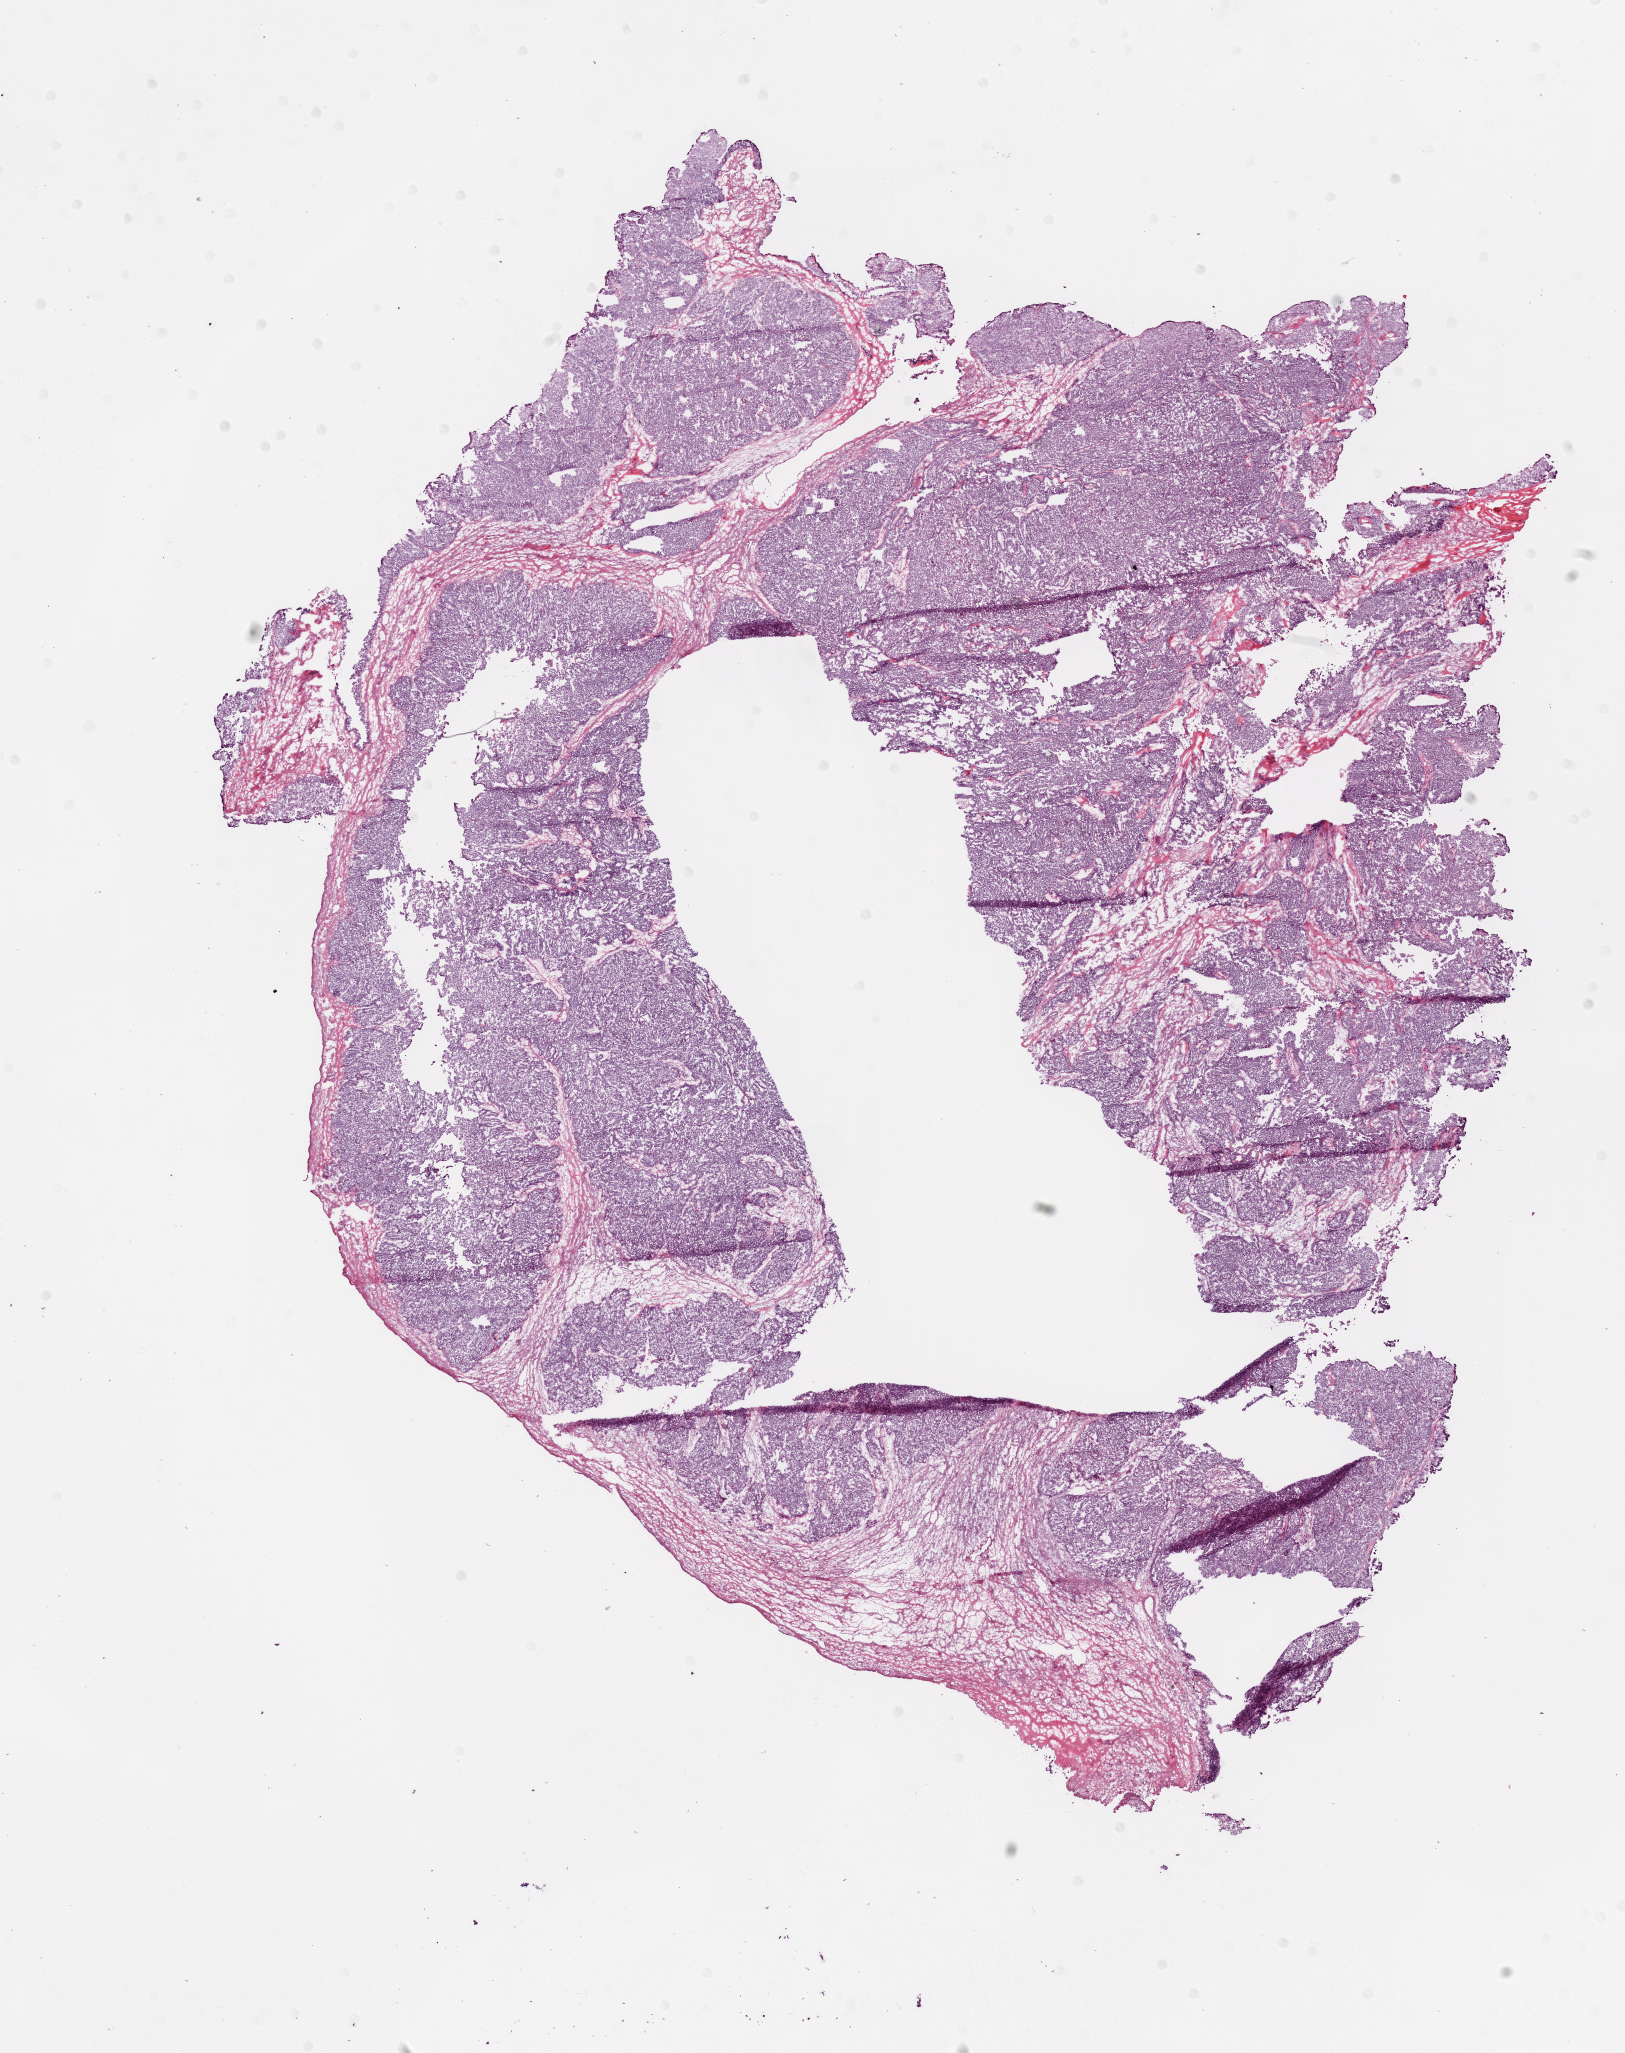
Whole-slide histology image, H&E-stained — a low-resolution overview of the entire scanned area, about 13.0 x 16.5 mm (slide scanned at 20x), frozen section from the bottom of the tissue portion, ovary, primary tumour sample. Female patient; age at initial diagnosis 56 years. Histologic grade: G2 (moderately differentiated). Pathologist review of this section (percent, as recorded): tumour cells 98%, tumour nuclei 95%, normal cells 0%, stromal cells 0%, necrosis 2%.
FIGO stage: IIIC. Diagnosis: Serous cystadenocarcinoma, NOS. Laterality: bilateral.